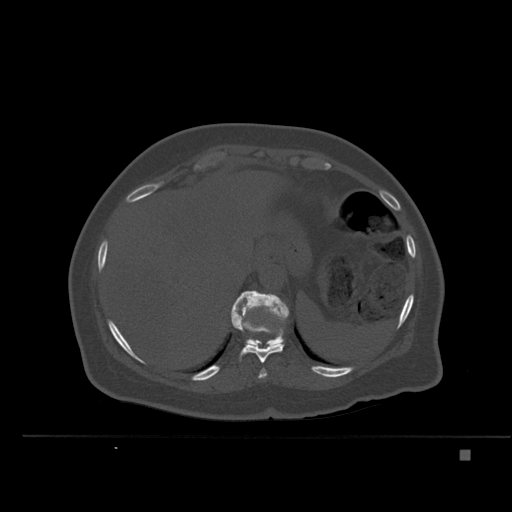
CT including the spine, one axial slice. Position 280 of 477 along the scan axis. Bone window (W 1800 / L 400 HU). 1.5 mm slice thickness. 512 × 512 image matrix. Female patient, age 74 years. From the clinical record (not read from this slice): primary cancer: colon.
Structures marked on this image (semi-automatically segmented with operator editing):
- T10 vertebra: box from (x=232, y=310) to (x=284, y=363) px
- T11 vertebra: (x=231, y=290)–(x=289, y=347)
- T9 vertebra: (x=258, y=369)–(x=267, y=379)